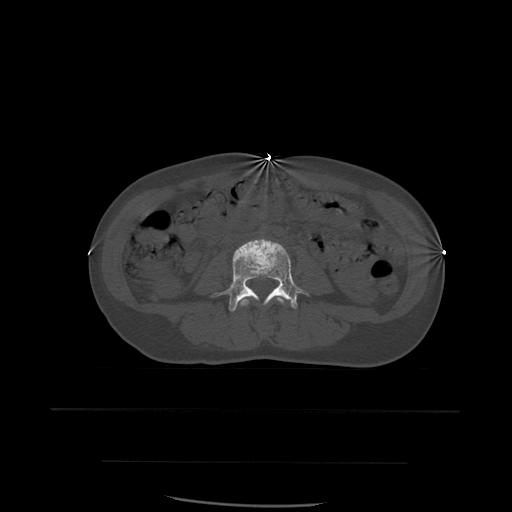
CT including the spine, one axial slice. Position 178 of 574 along the scan axis. Bone window (W 1800 / L 400 HU). 1.25 mm slice thickness. 512 × 512 image matrix, field of view 392 × 392 mm. Patient age 48 years. From the clinical record (not read from this slice): primary cancer: lung; vertebrae with lytic lesions (as recorded): T11.
Annotated regions visible in this slice (semi-automatic segmentation, software-assisted and operator-edited):
- L3 vertebra: bounding box (x1, y1, x2, y2) in pixels: (240, 297, 290, 325)
- L4 vertebra: (212, 239, 308, 312)